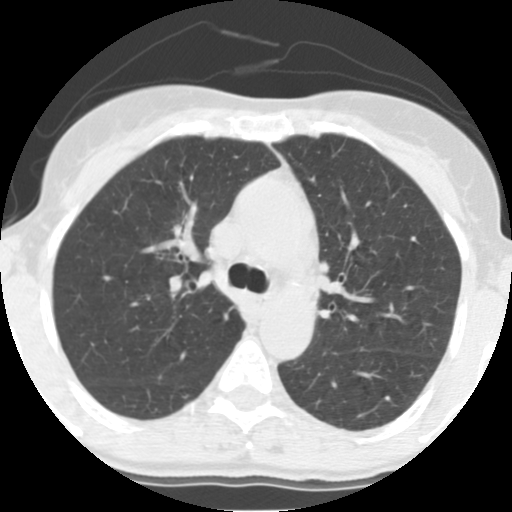
Low-dose screening chest CT, one axial slice; slice 95 of 140 in the series (ordered by position); lung window (W 1500 / L -600 HU); 2.5 mm slice thickness; 512 × 512 image matrix, field of view 280 × 280 mm.
Outlined on this slice (expert manual segmentation):
- lesion 1 (tumor, upper lobe of right lung): bounding box [x1, y1, x2, y2] px = [172, 225, 182, 239]